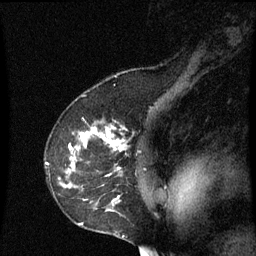
Breast MRI (dynamic contrast-enhanced), one sagittal slice; position 46 of 60 along the scan axis; dynamic contrast-enhanced series, image 2 of 3 at this slice position (ordered by acquisition); 1.5 T; TE 4.2 ms, TR 8.9 ms; 256 × 256 image matrix. Female patient, age 53 years. Case-level facts recorded for this patient, not image findings: setting: breast cancer imaged before/during neoadjuvant chemotherapy; receptor status: HR-positive, HER2-negative.
Annotated regions visible in this slice (semi-automatic segmentation, software-assisted and operator-edited):
- analysis volume of interest (the breast-tissue region the enhancement analysis was run in; not a lesion): bounding box <46,128,157,229> (left, top, right, bottom; pixels)
- tumour enhancement mask (voxels above the 70 % enhancement threshold inside the analysis volume of interest): <66,128,127,177>